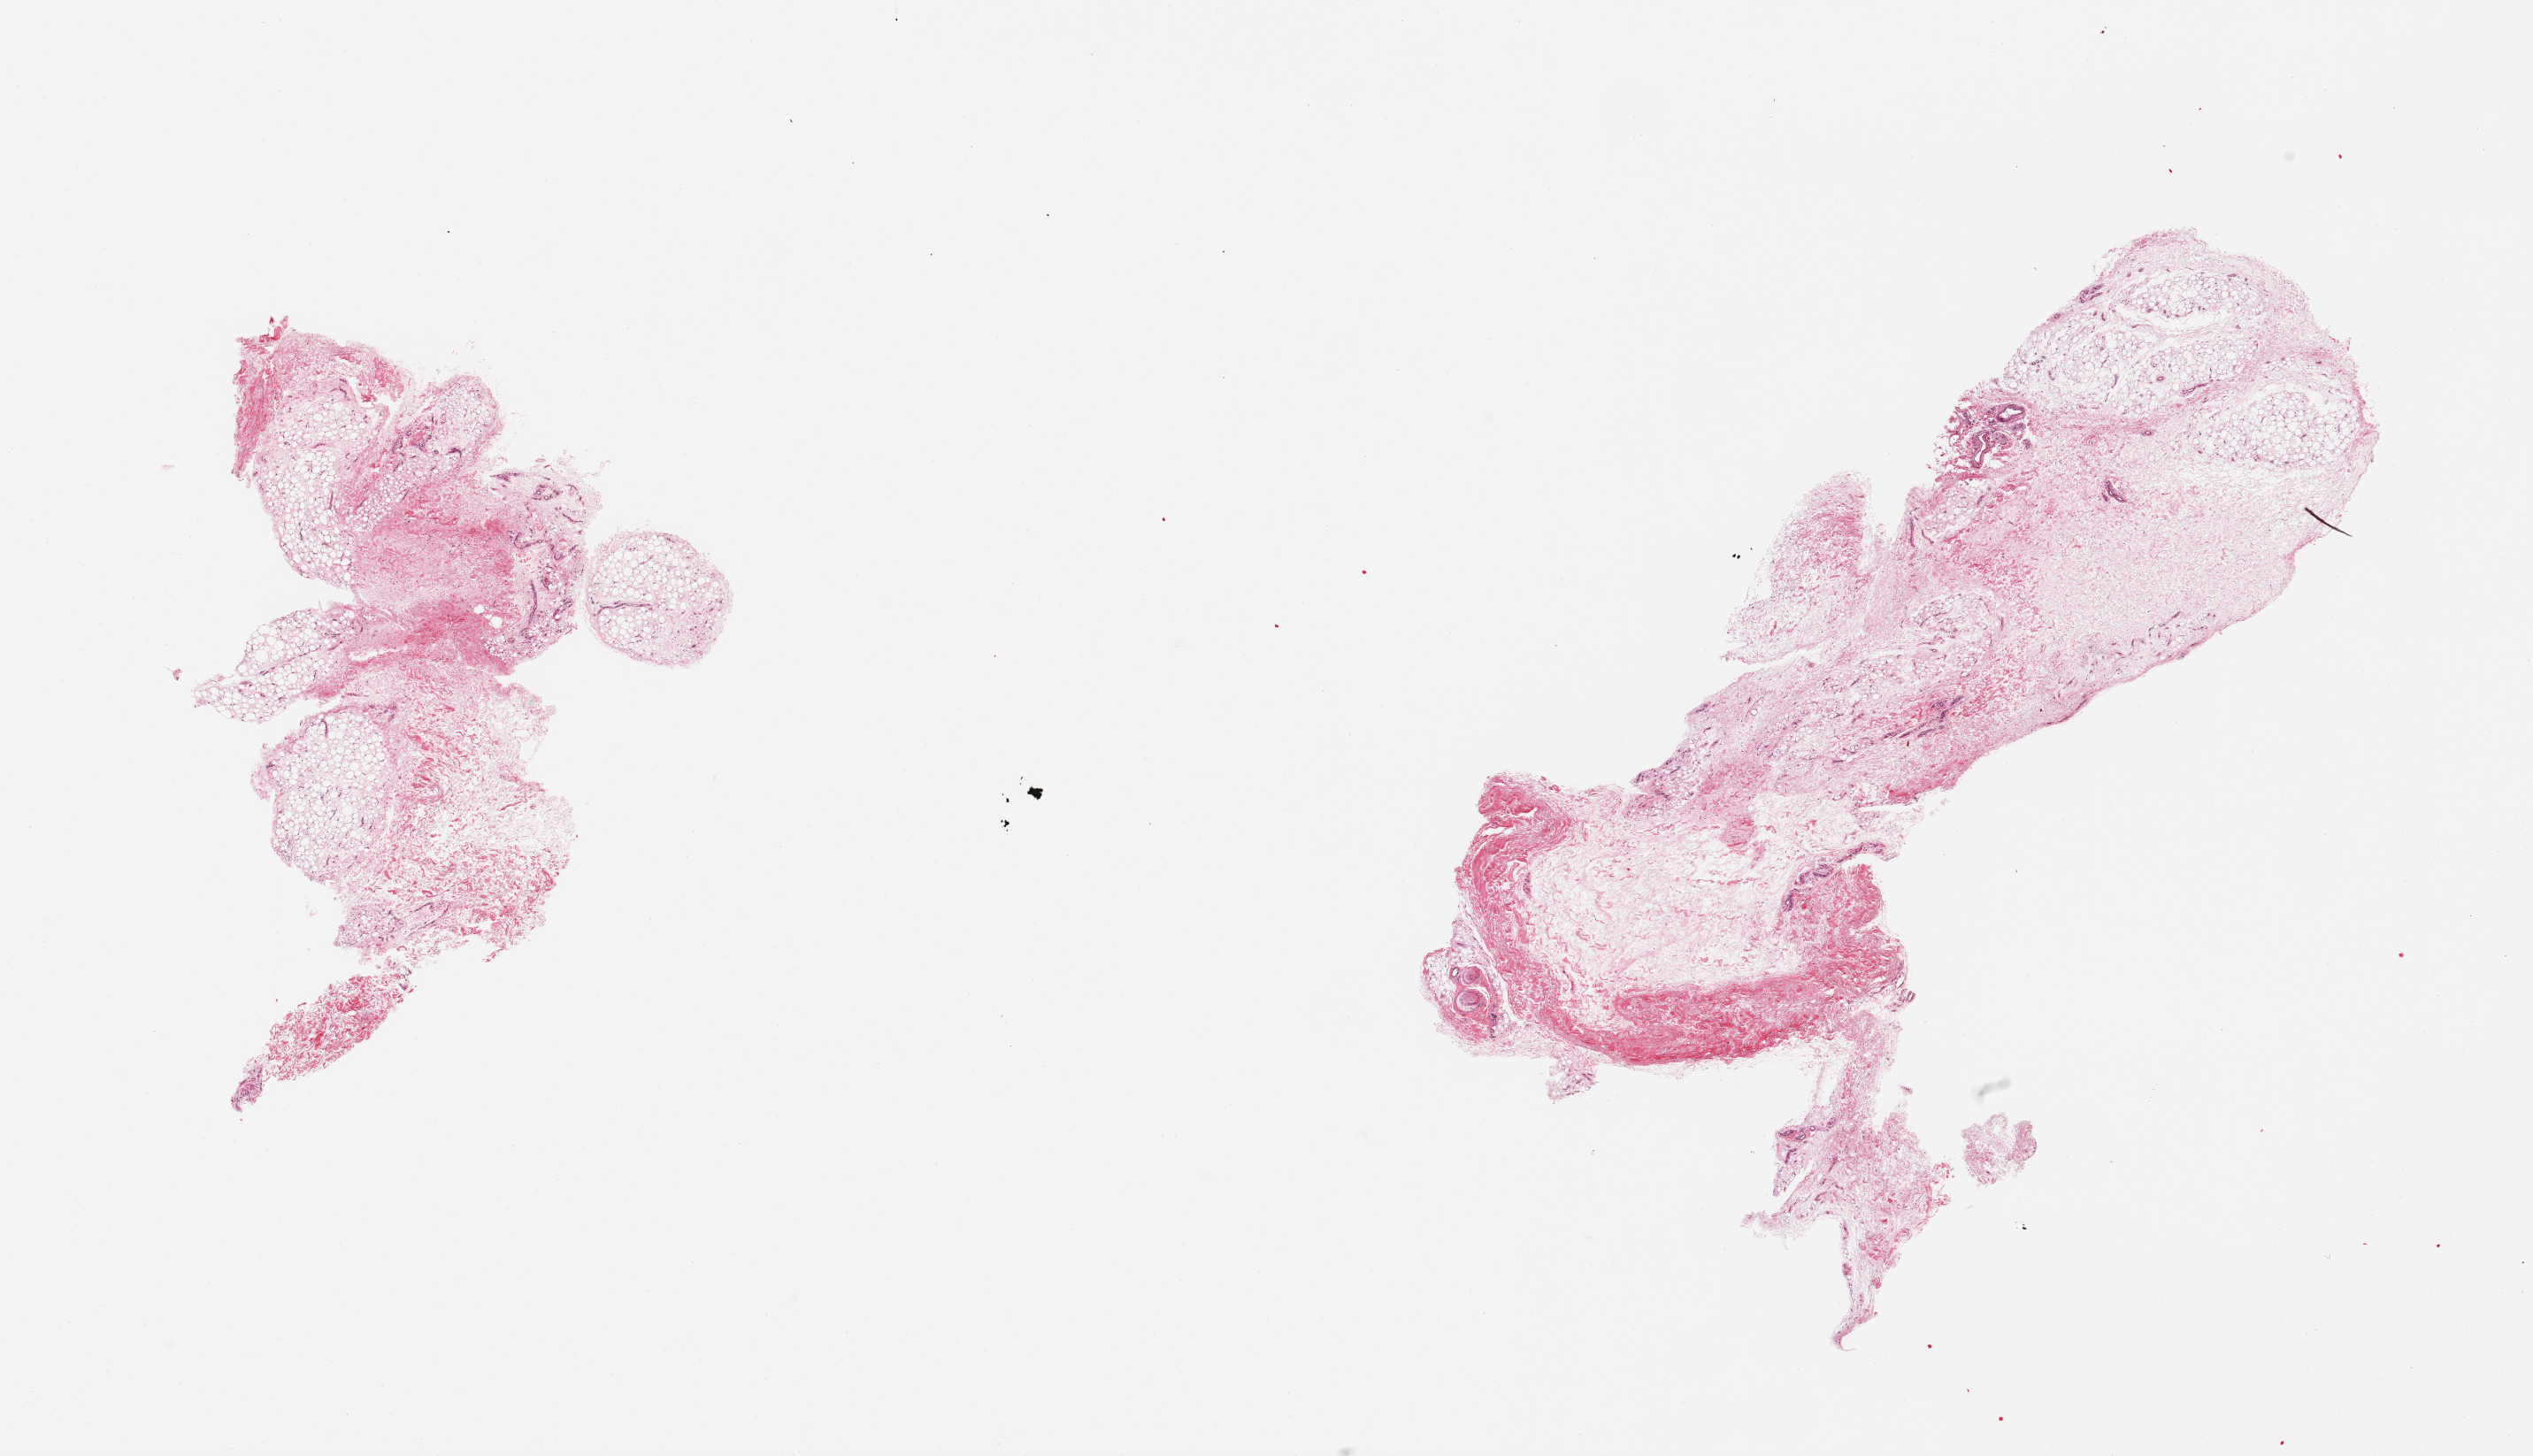
Digitized haematoxylin and eosin-stained section — shown as a low-resolution overview of the whole scanned area (about 22.6 x 13.0 mm); PAXgene-fixed paraffin-embedded (PFPE) section; target tissue: adipose tissue; donor tissue sample. Donor: male.
Review note (as recorded): 2 pieces; only ~15 and 30% fat with significant fibrous/vascular/nerve tissue.